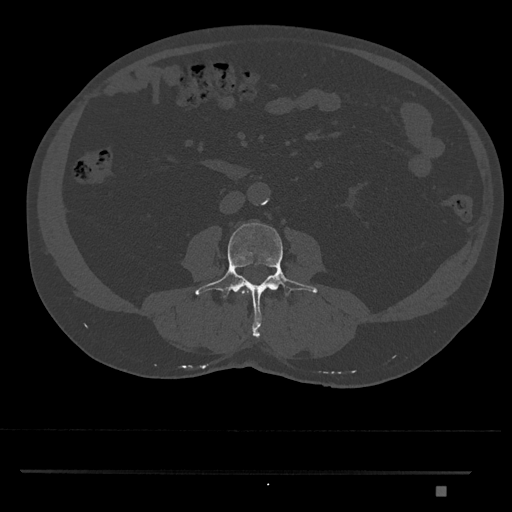
CT including the spine, one axial slice; position 683 of 1134 along the scan axis; reconstruction kernel Br40s/3; 120 kVp; bone window (W 1800 / L 400 HU); 512 × 512 image matrix, field of view 429 × 429 mm. Patient: male, 65 years. Case-level facts recorded for this patient, not image findings: primary cancer: prostate.
Outlined on this slice (semi-automatic segmentation, software-assisted and operator-edited):
- L2 vertebra: bounding box <241,290,247,295> (left, top, right, bottom; pixels)
- L3 vertebra: <195,222,318,338>